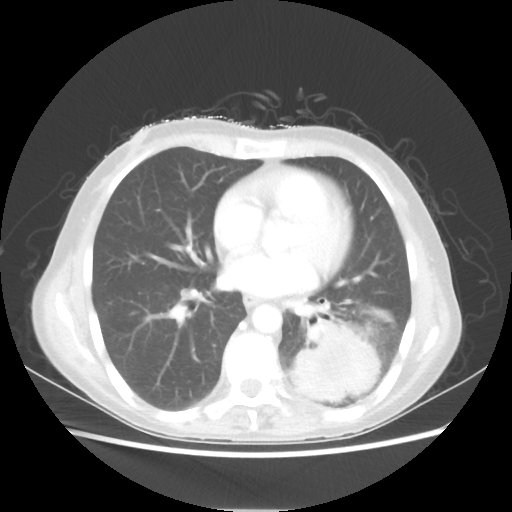
Chest CT, one axial slice; slice 25 of 56 in the series (ordered by position); reconstruction kernel STANDARD; 80 kVp; lung window (W 1500 / L -600 HU); 5 mm slice thickness; 512 × 512 image matrix, field of view 360 × 360 mm. Female patient, age 53 years. From the clinical record (not read from this slice): clinical TNM (as recorded): T3 N0 M0.
Annotated regions visible in this slice (bounding box drawn by a radiologist):
- lung tumour (recorded histology: adenocarcinoma): bounding box (x1, y1, x2, y2) in pixels: (287, 321, 380, 403)